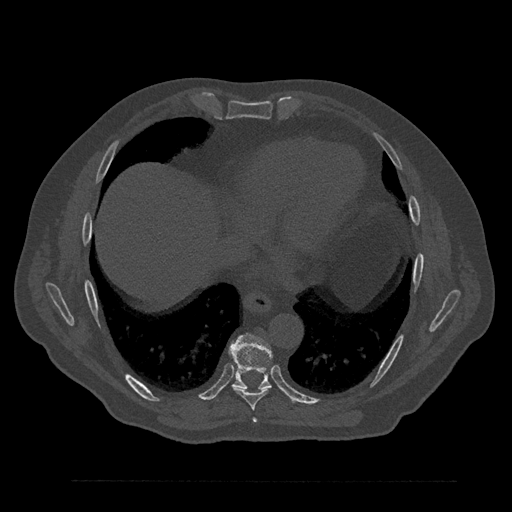
CT including the spine, one axial slice; slice 434 of 797 in the series (ordered by position); reconstruction kernel Br40s/3; 120 kVp; bone window (W 1800 / L 400 HU); 0.5 mm slice thickness; 512 × 512 image matrix, field of view 430 × 430 mm. Male patient, age 61 years. Case-level facts recorded for this patient, not image findings: primary cancer: prostate.
Annotated regions visible in this slice (semi-automatic segmentation, software-assisted and operator-edited):
- T7 vertebra: bounding box <253,418,257,423> (left, top, right, bottom; pixels)
- T8 vertebra: <231,386,272,410>
- T9 vertebra: <229,334,272,389>